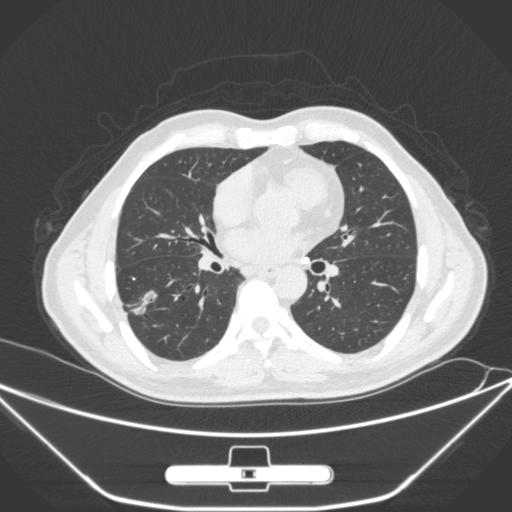
Chest CT, one axial slice. Slice 142 of 310 in the series (ordered by position). 120 kVp. Lung window (W 1500 / L -600 HU). 1 mm slice thickness. 512 × 512 image matrix, field of view 398 × 398 mm. Male patient, age 71 years. From the clinical record (not read from this slice): clinical TNM (as recorded): T1c N0 M0; histopathological grade: G2.
Structures marked on this image (rectangle marked by the reading radiologist):
- lung tumour (recorded histology: adenocarcinoma): box from (x=125, y=282) to (x=162, y=317) px